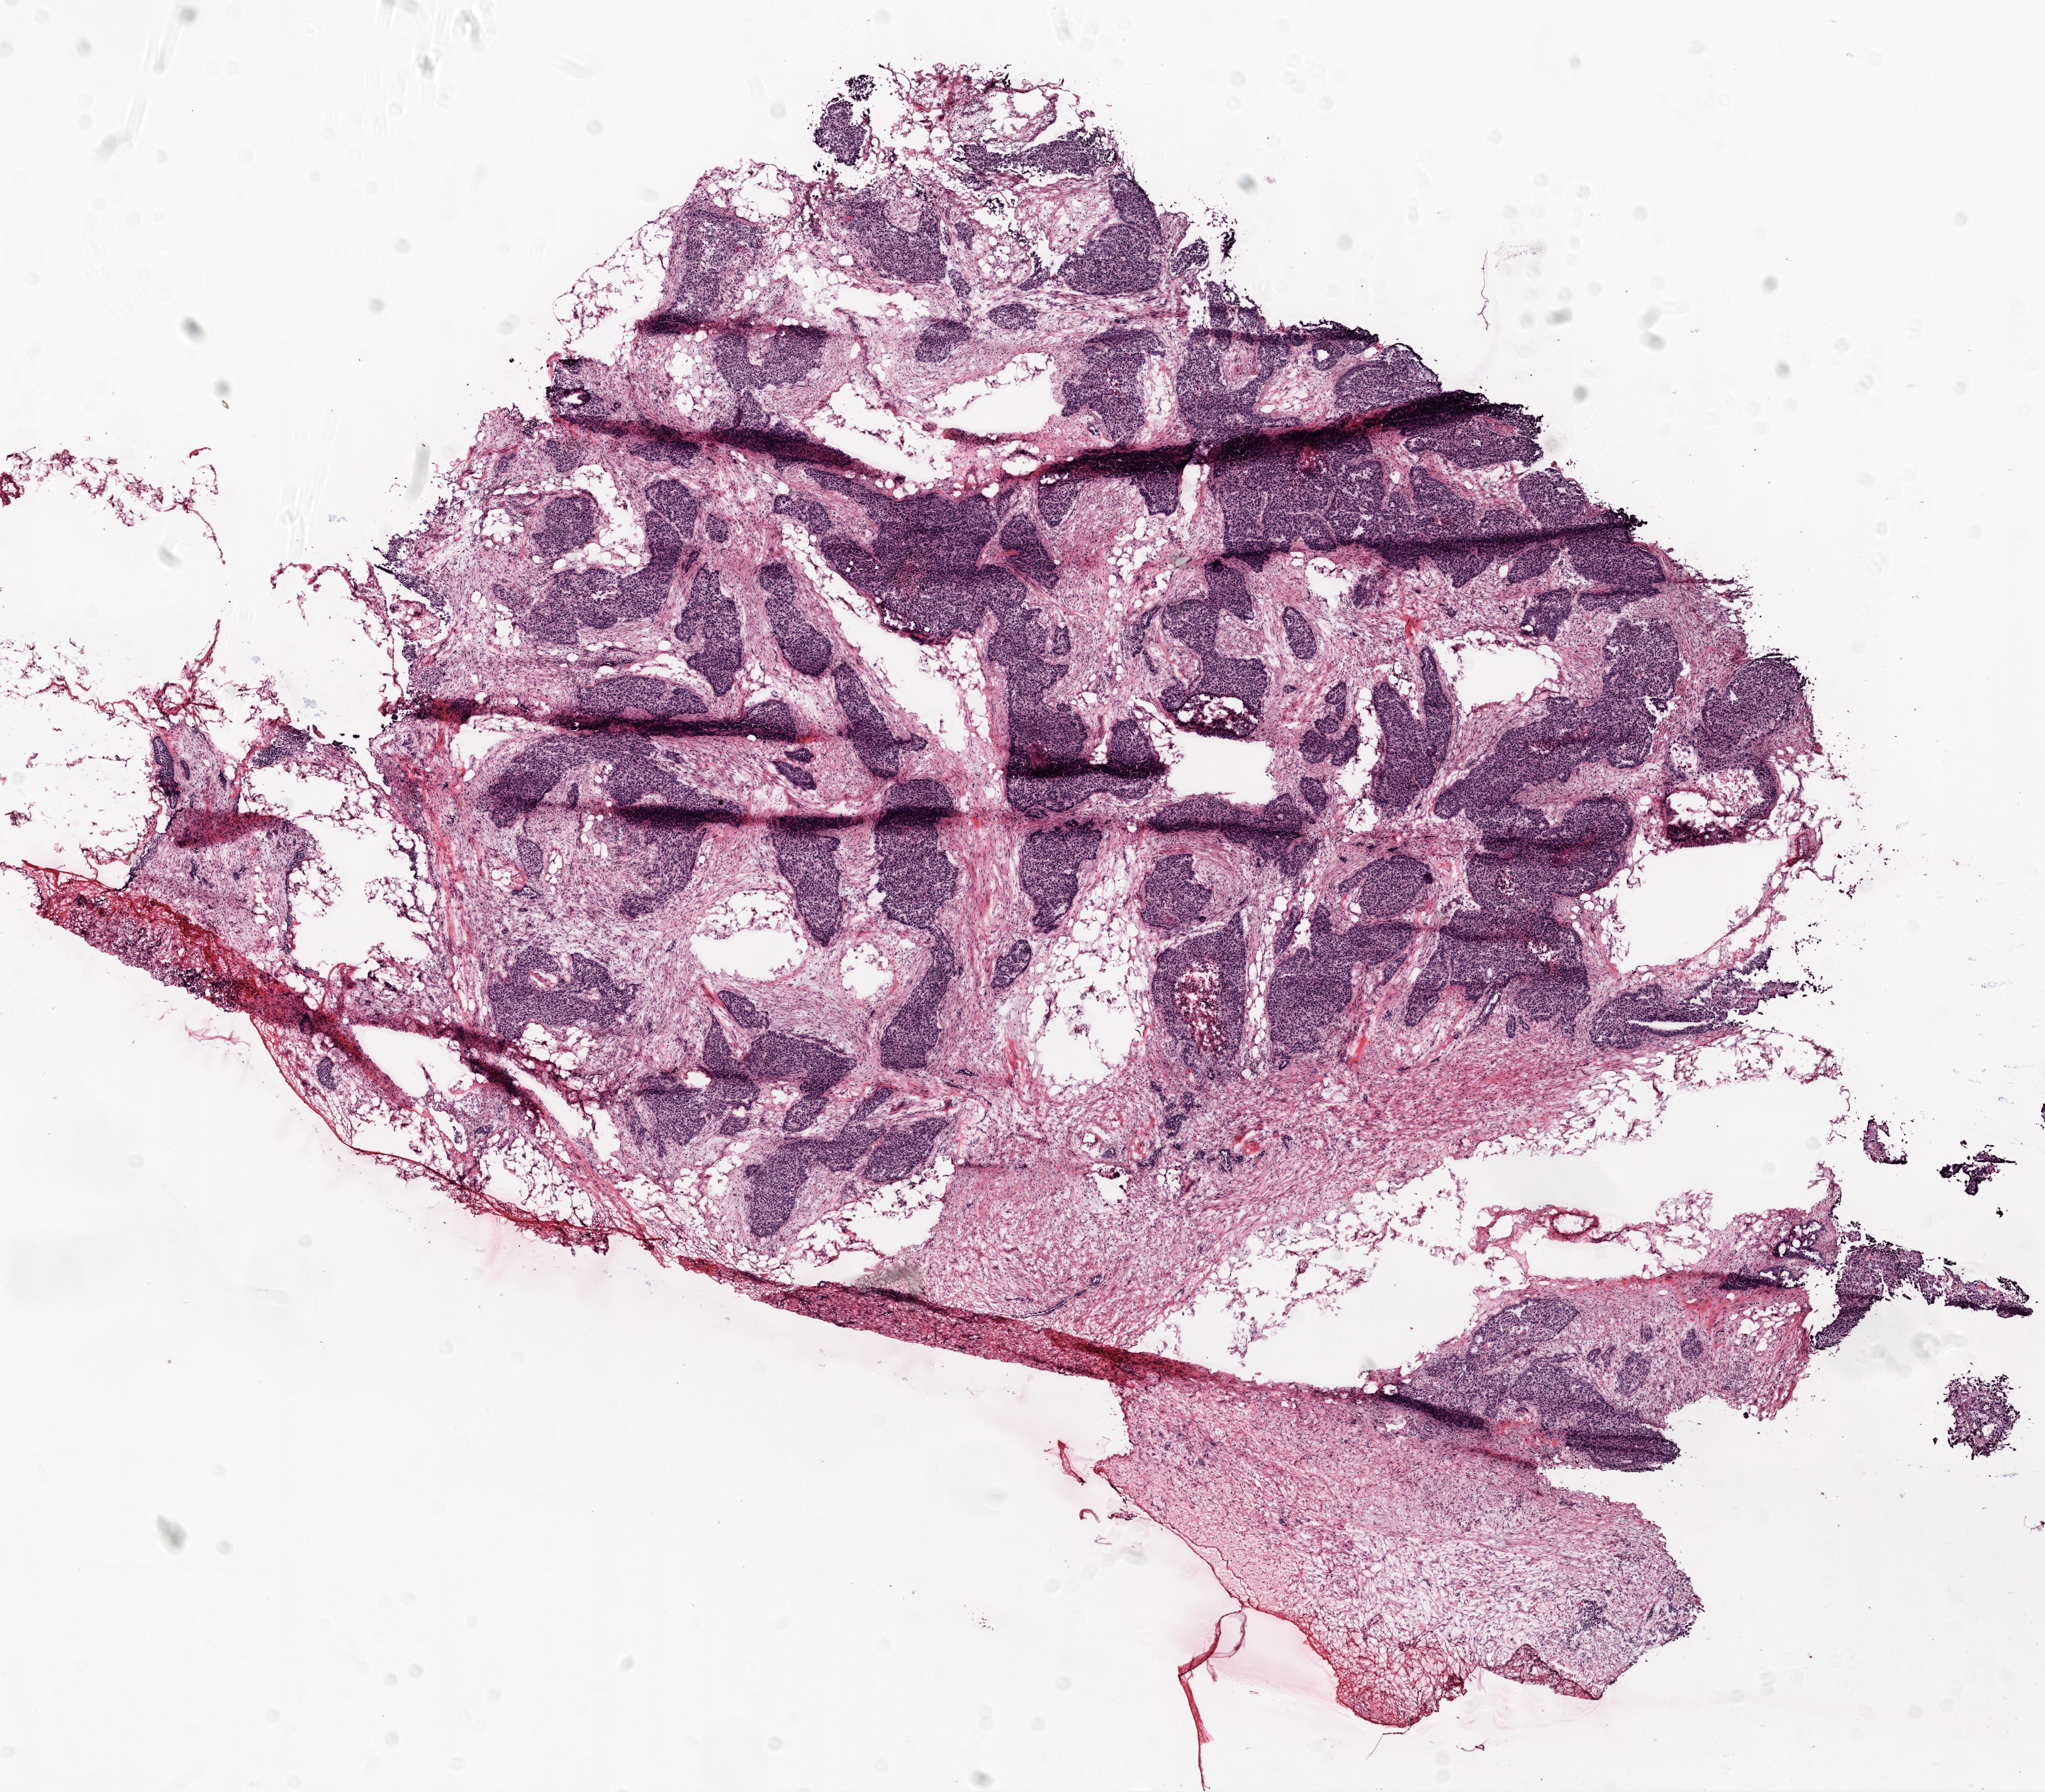
Whole-slide histology image, H&E-stained — low-resolution overview of the scanned area, about 13.0 x 11.4 mm. Frozen section from the top of the tissue portion. Primary tumour sample from the ovary. Female, age 53 years at initial diagnosis. Histologic grade: G3 (poorly differentiated). Slide review estimates, as recorded: tumour cells 50%, tumour nuclei 70%, normal cells 0%, stromal cells 45%, necrosis 5%.
Pathologic diagnosis: Serous cystadenocarcinoma, NOS. FIGO stage: IIIC.